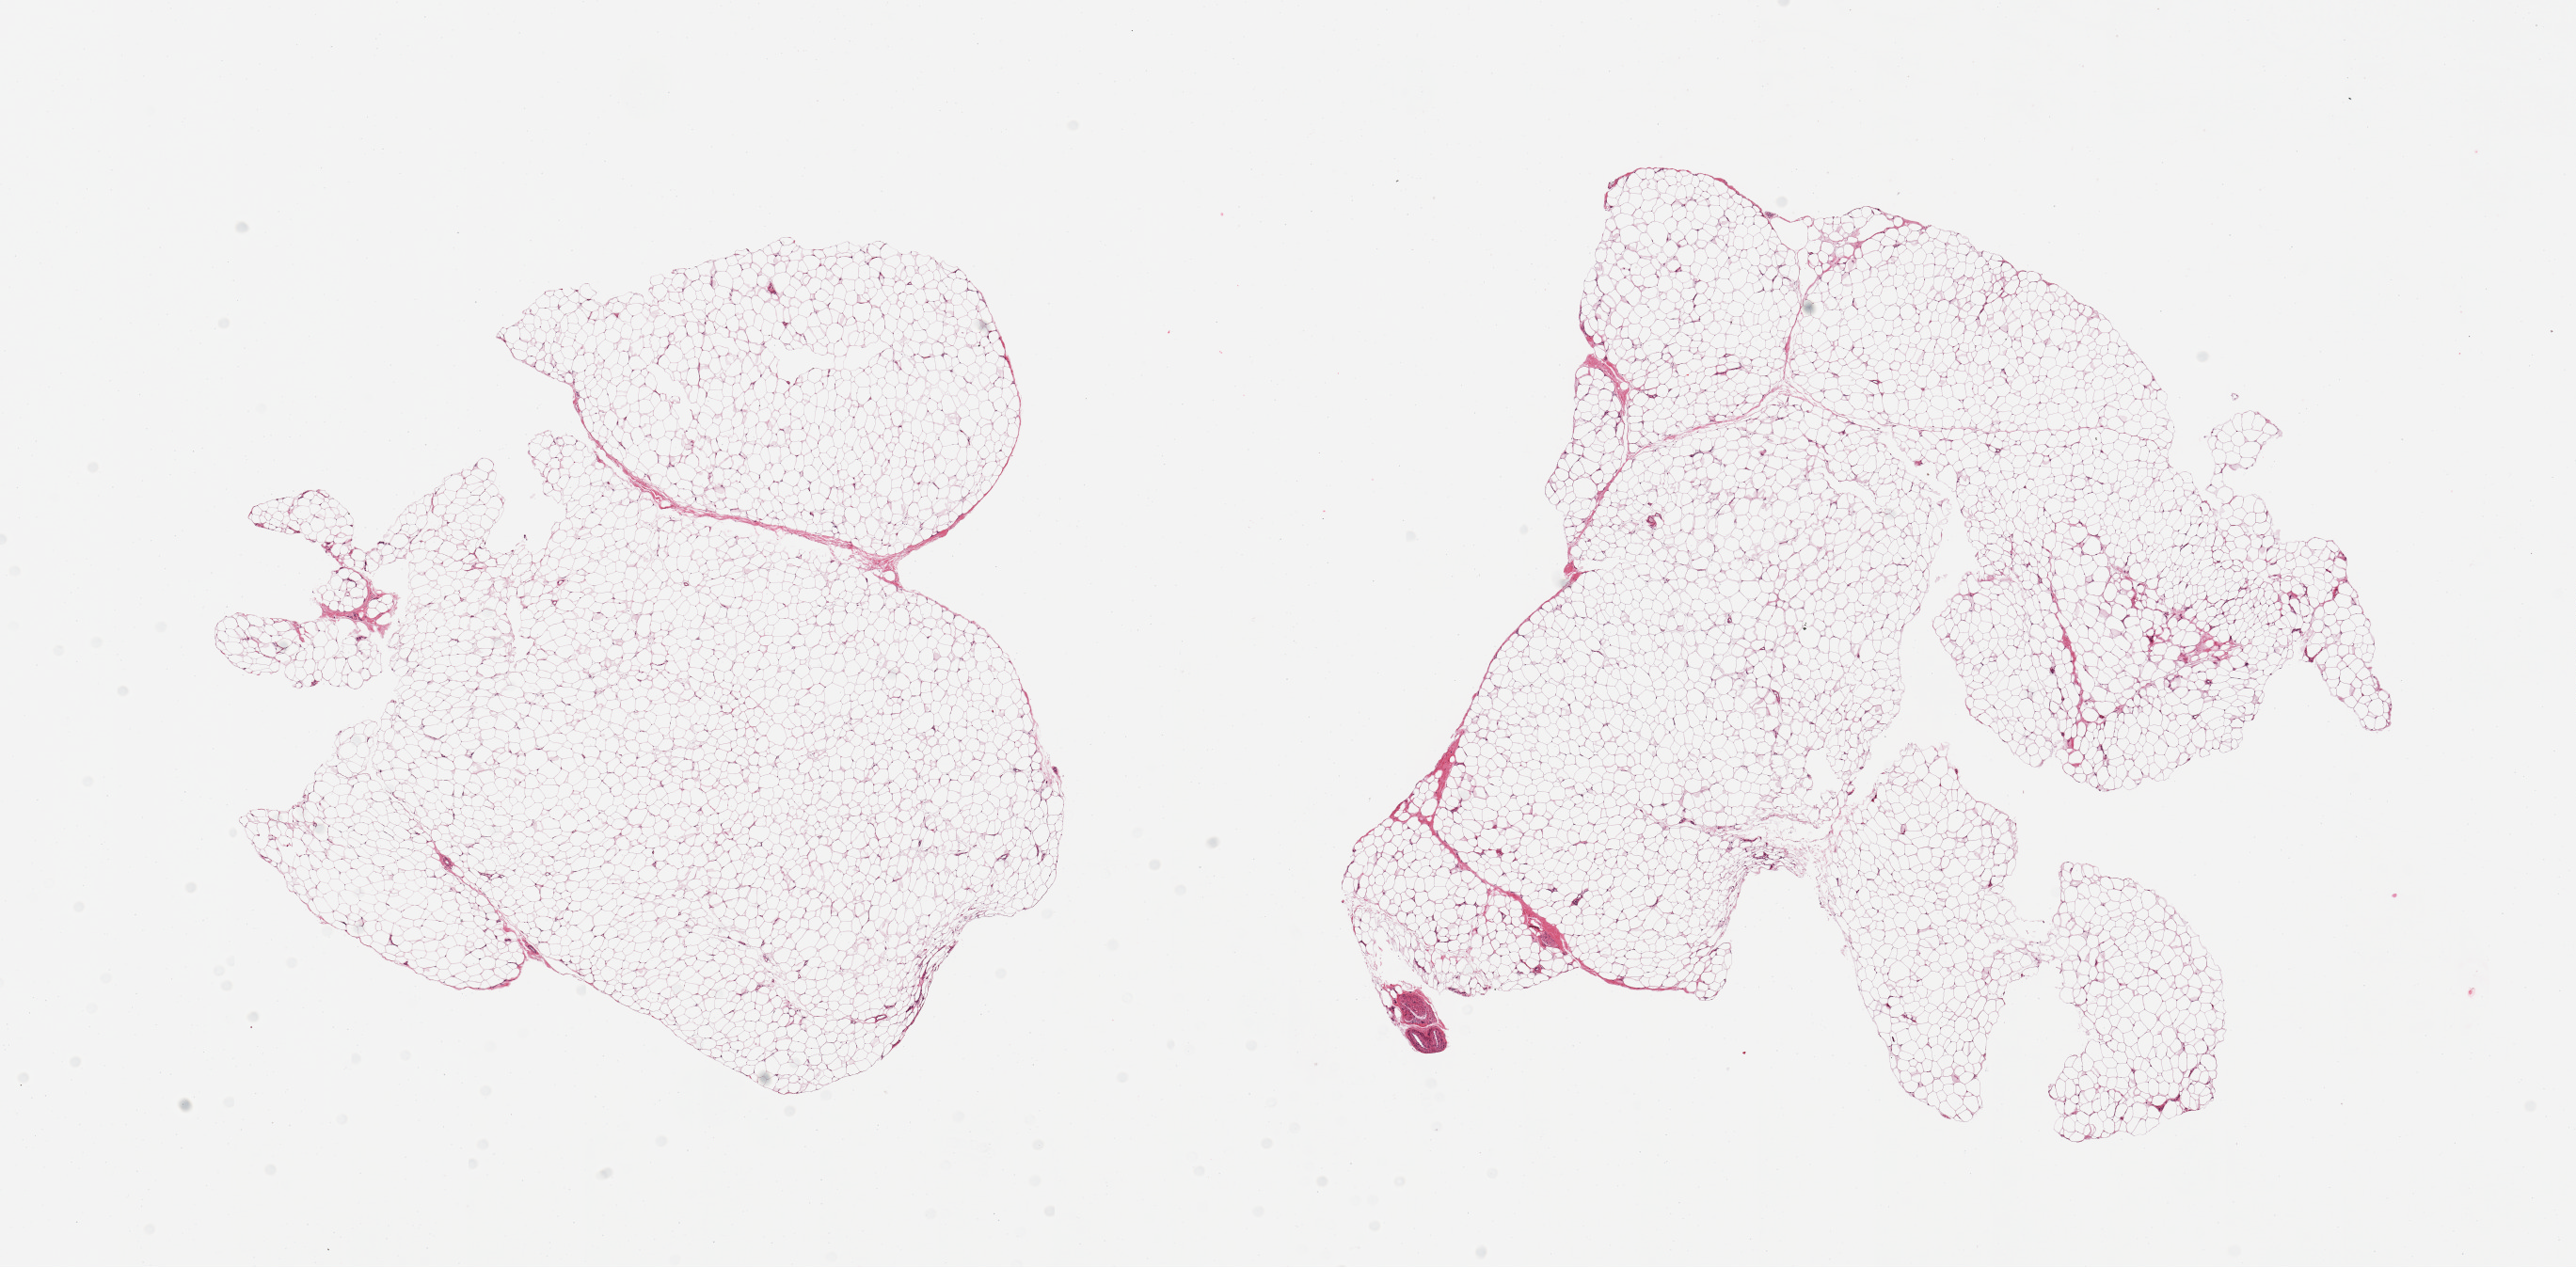
Digitized H&E-stained section, brightfield, low-resolution overview of the scanned area, about 21.7 x 10.7 mm (from a 20x scan), PAXgene-fixed paraffin-embedded (PFPE) section, target tissue: adipose tissue, tissue donor sample. Donor: female.
Review note (as recorded): 2 pieces, minimal fascia/vascular elements.